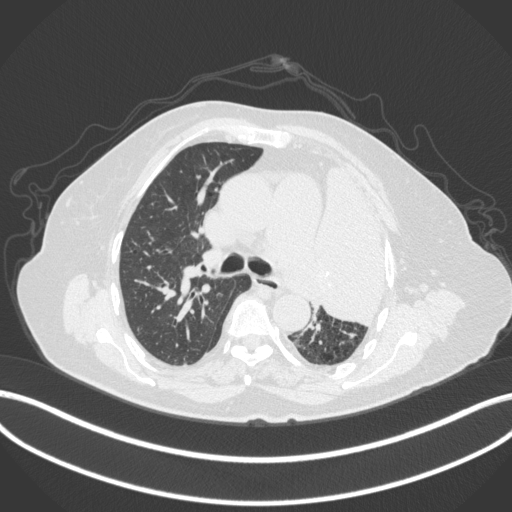
Chest CT, one axial slice. Reconstruction kernel B31f. Lung window (W 1500 / L -600 HU). 1 mm slice thickness. 512 × 512 image matrix, field of view 400 × 400 mm. Patient: female, 75 years. Case-level facts recorded for this patient, not image findings: clinical TNM (as recorded): T3 N3 M1.
Structures marked on this image (rectangle marked by the reading radiologist):
- lung tumour (recorded histology: adenocarcinoma): box from (x=310, y=153) to (x=405, y=329) px